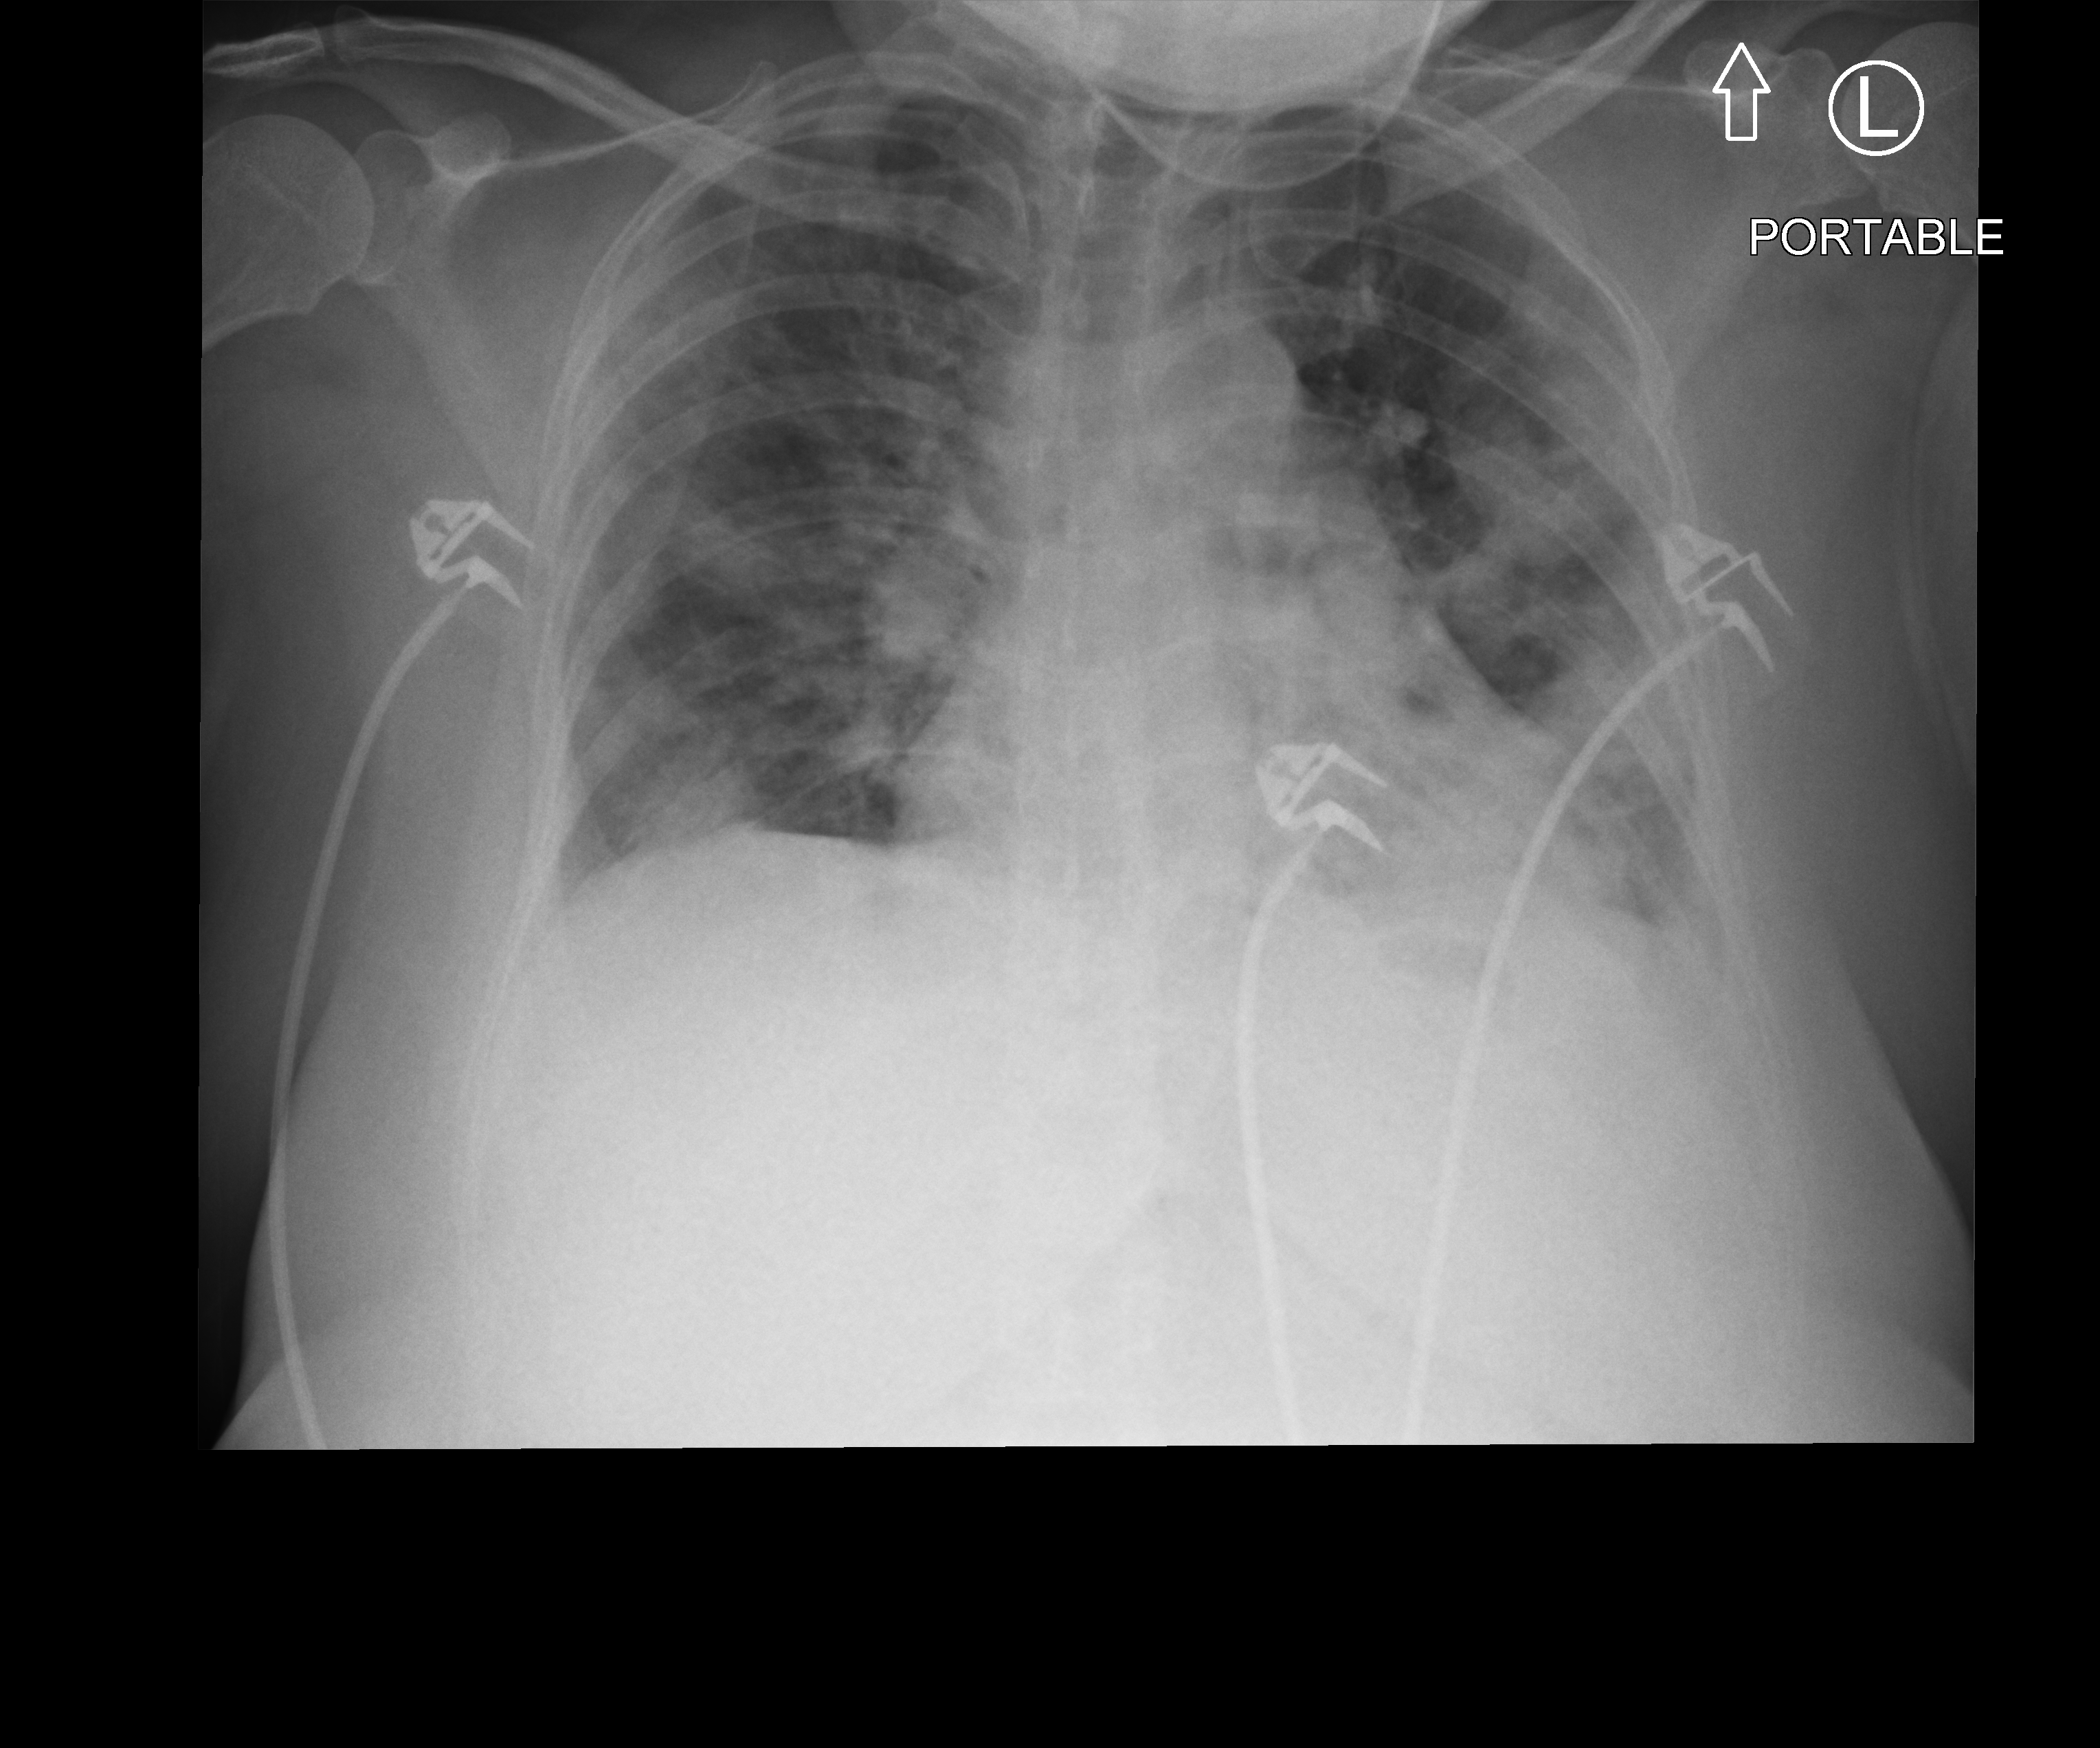
Portable chest radiograph, anteroposterior (AP) projection. Adult patient hospitalised with COVID-19, age 18–59 years.
Hospital-stay facts (about this admission, not read from this image; timing relative to this image not recorded):
- length of hospital stay: 10 days